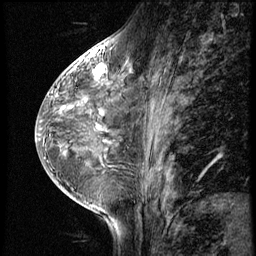
Breast MRI (dynamic contrast-enhanced), one sagittal slice. Position 27 of 56 along the scan axis. 3 images stored at this slice position (order not interpretable as contrast timing). 1.5 T. TE 4.2 ms, TR 8.9 ms. 256 × 256 image matrix. Female patient, age 38 years. From the clinical record (not read from this slice): setting: breast cancer imaged before/during neoadjuvant chemotherapy; receptor status: triple-negative.
Structures marked on this image (semi-automatically segmented with operator editing):
- analysis volume of interest (the breast-tissue region the enhancement analysis was run in; not a lesion): bounding box <88,60,110,84> (left, top, right, bottom; pixels)
- tumour enhancement mask (voxels above the 140 % enhancement threshold inside the analysis volume of interest): <95,65,105,73>